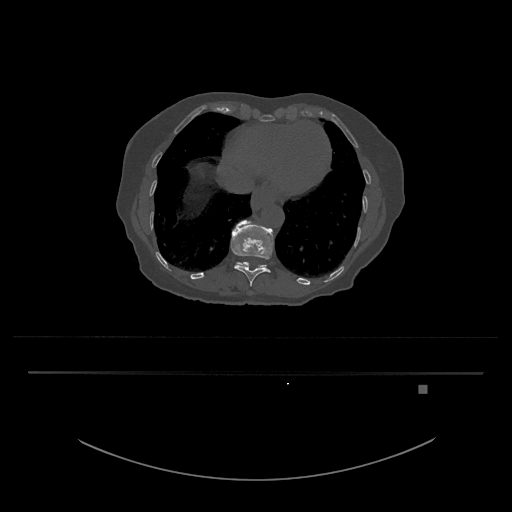
CT including the spine, one axial slice. Slice 655 of 797 in the series (ordered by position). Bone window (W 1800 / L 400 HU). 0.5 mm slice thickness. 512 × 512 image matrix, field of view 500 × 500 mm. Patient: female, 57 years. From the clinical record (not read from this slice): primary cancer: cervical.
Outlined on this slice (semi-automatic segmentation, software-assisted and operator-edited):
- T11 vertebra: bounding box <231,220,274,287> (left, top, right, bottom; pixels)
- T12 vertebra: <236,262,267,268>